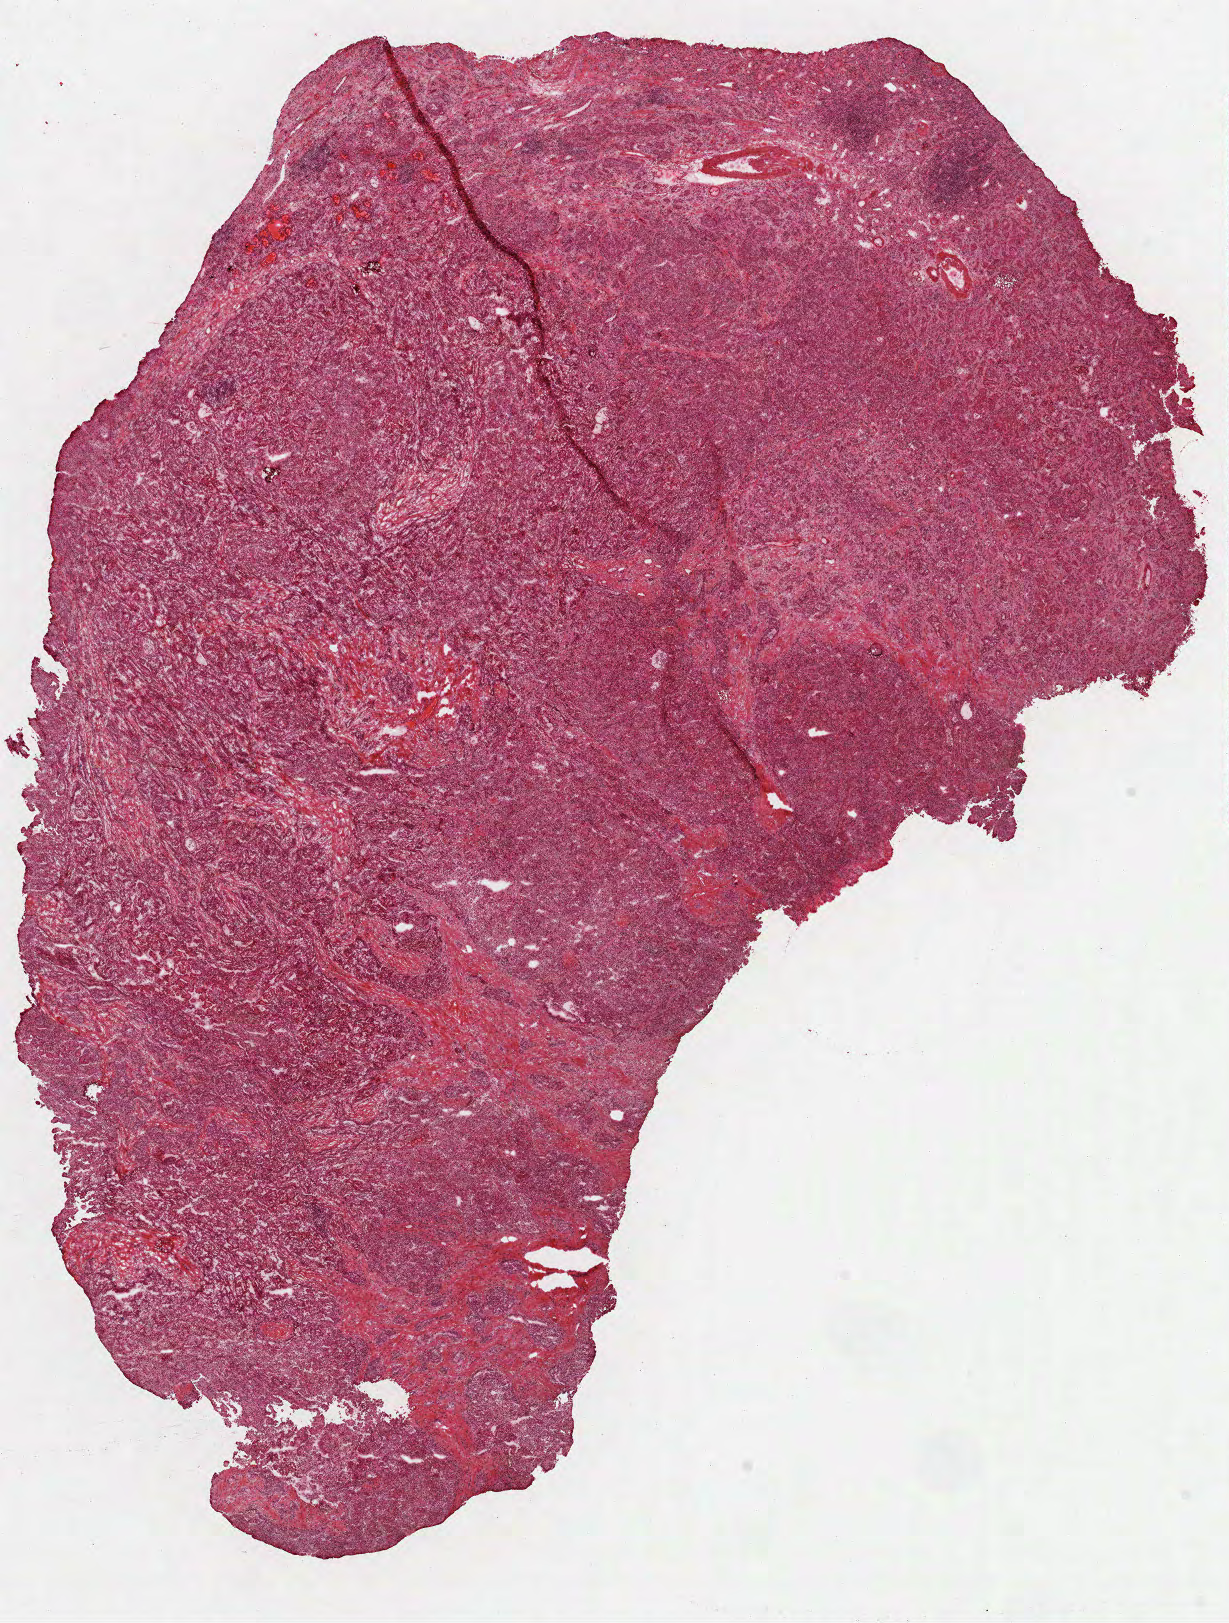
Hematoxylin and eosin (H&E) stained whole-slide image, shown as a low-resolution overview of the whole scanned area (about 9.9 x 13.1 mm, acquisition: 40x scan); frozen section; kidney, primary tumour sample. Female, age 45 years at initial diagnosis. Slide review estimates, as recorded: tumour cells 100%, tumour nuclei 65%, normal cells 0%, stromal cells 0%, necrosis 0%. Inflammatory infiltration, as recorded: lymphocyte infiltration 3%, monocyte infiltration 0%, neutrophil infiltration 30%.
• pathologic diagnosis: Papillary adenocarcinoma, NOS
• laterality: right
• AJCC pathologic stage: I (6th edition)